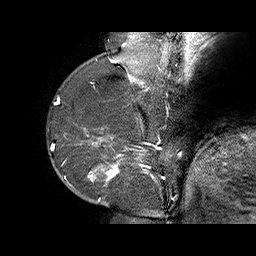
Breast MRI (dynamic contrast-enhanced), one sagittal slice; slice 16 of 70 in the series (ordered by position); dynamic contrast-enhanced series, time point 2 of 6 at this slice position (early post-contrast); 1.5 T; TE 4.5 ms, TR 32.4 ms; 256 × 256 image matrix, field of view 180 × 180 mm. Female patient. From the clinical record (not read from this slice): setting: breast cancer imaged before/during neoadjuvant chemotherapy; receptor status: HR-positive, HER2-negative.
Outlined on this slice (semi-automatic segmentation, software-assisted and operator-edited):
- analysis volume of interest (the breast-tissue region the enhancement analysis was run in; not a lesion): bounding box [x1, y1, x2, y2] px = [71, 128, 159, 202]
- tumour enhancement mask (voxels above the 100 % enhancement threshold inside the analysis volume of interest): [80, 128, 156, 201]